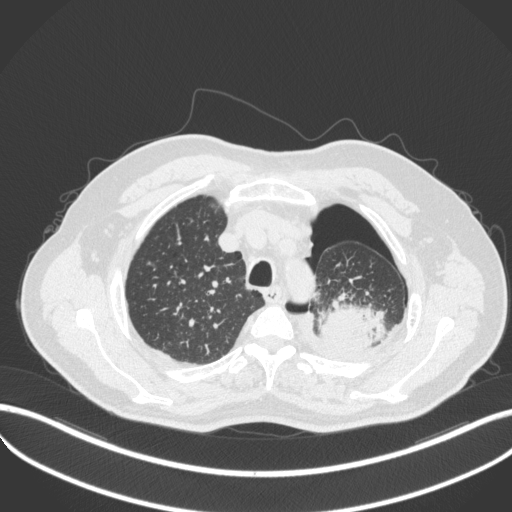
Chest CT, one axial slice. Position 407 of 466 along the scan axis. Reconstruction kernel B31f. 120 kVp. Lung window (W 1500 / L -600 HU). 512 × 512 image matrix, field of view 400 × 400 mm. Male patient, age 76 years. From the clinical record (not read from this slice): clinical TNM (as recorded): T3 N0 M1b.
Structures marked on this image (rectangle marked by the reading radiologist):
- lung tumour (recorded histology: adenocarcinoma): bounding box <316,300,391,353> (left, top, right, bottom; pixels)